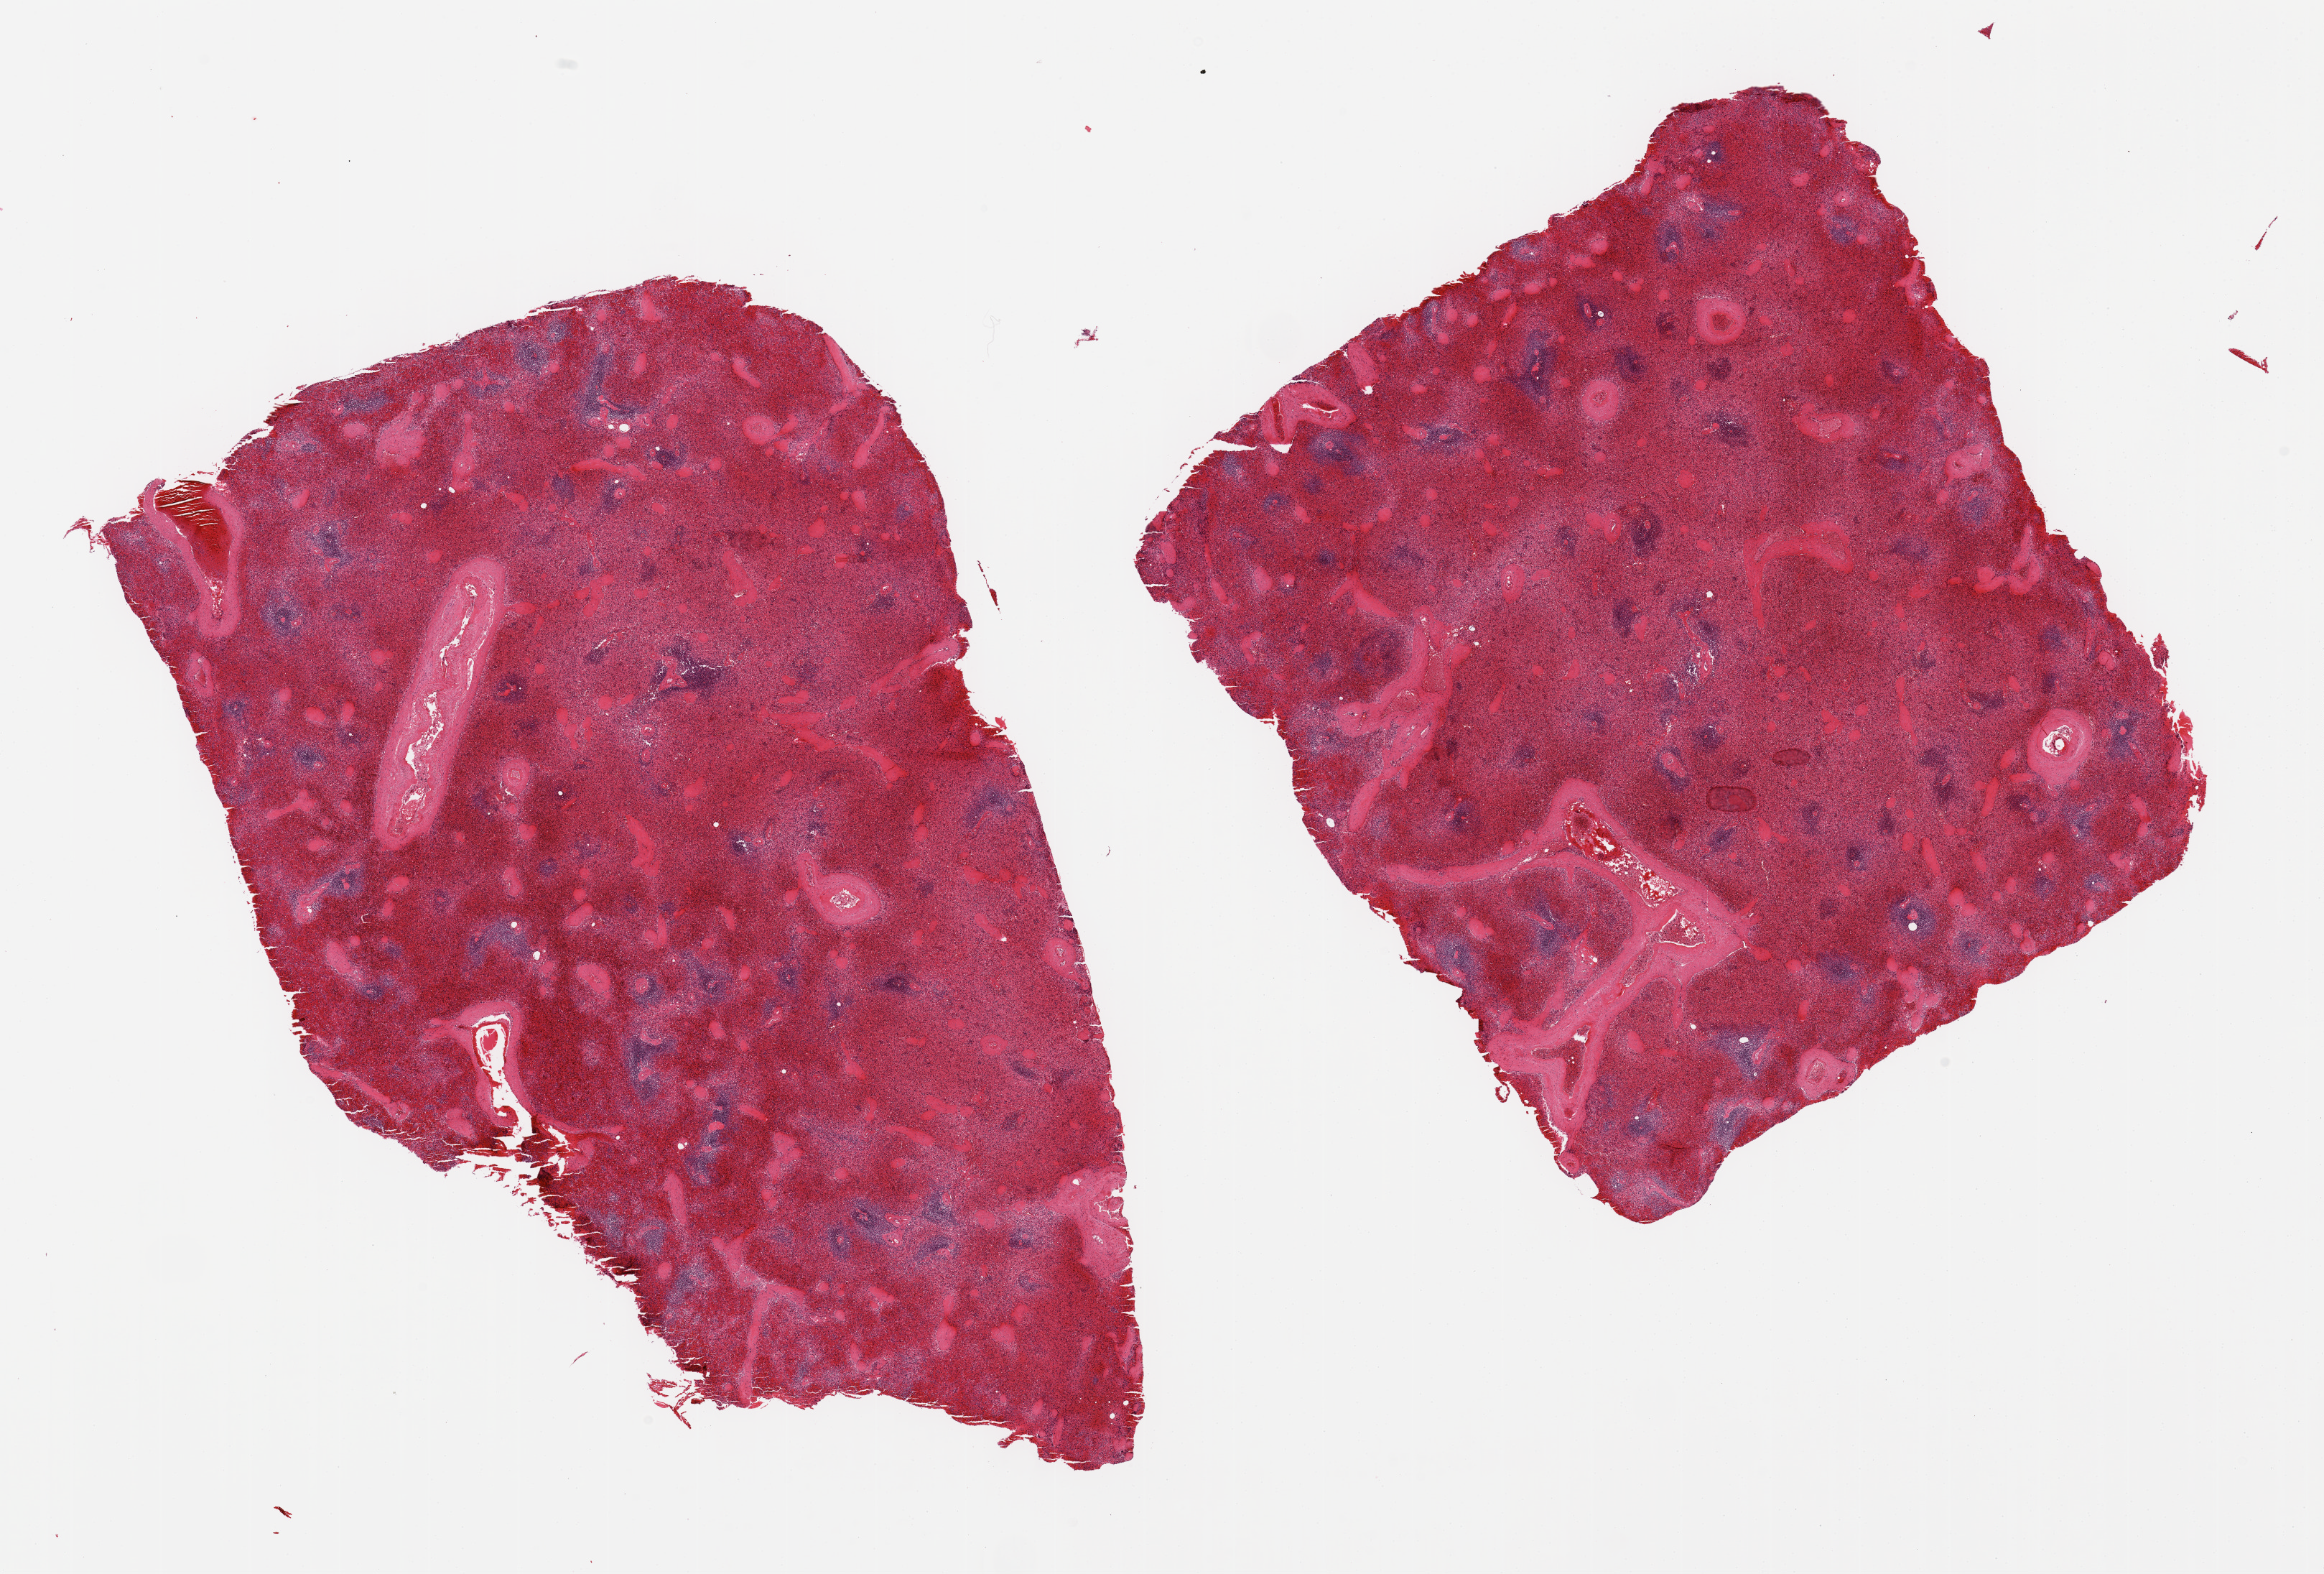
Haematoxylin and eosin whole-slide image, brightfield — a low-resolution overview of the entire scanned area, about 25.6 x 17.3 mm. PAXgene-fixed paraffin-embedded (PFPE) section. Target tissue: spleen. Tissue donor sample. Donor sex: male.
Review note (as recorded): 2 pieces; severe congestion.